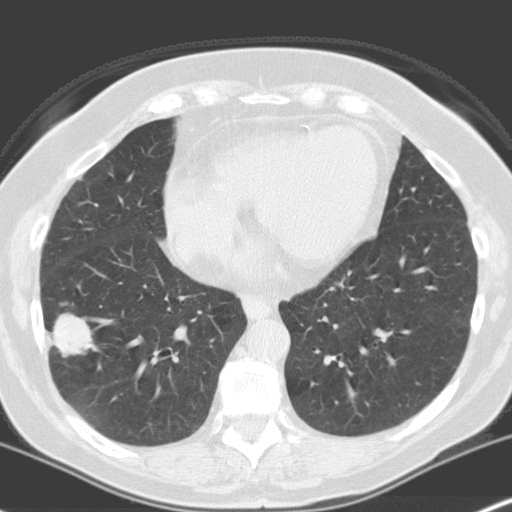
Chest CT (low-dose screening protocol), one axial image. First (baseline) screen. Lung window (W 1500 / L -600 HU). 3.2 mm slice thickness. Standard (soft-tissue) reconstruction kernel (C). 120 kVp. 512 × 512 image matrix, field of view 316 × 316 mm. Female participant, aged 70 years at enrolment.
Expert reader's lesion annotation, bounding box <33,303,101,372> (left, top, right, bottom; pixels). The screening reader recorded 4 non-calcified nodules or masses ≥4 mm on this exam; which of them this box marks is not recorded. Later outcome: lung cancer diagnosed 28 days after this screen — adenocarcinoma, NOS, right lower lobe, moderately differentiated (G2), stage IV (AJCC 6th edition), 28 mm at pathology.